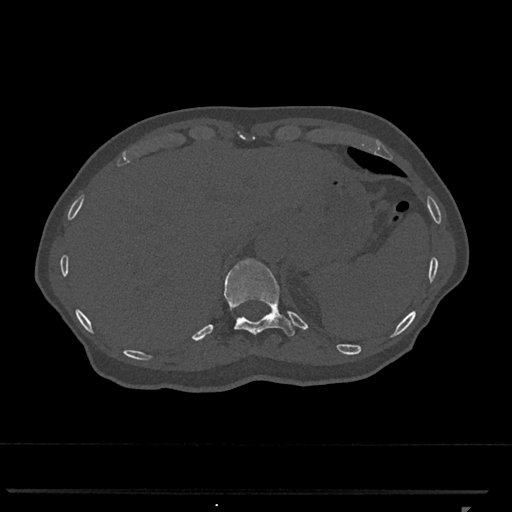
CT including the spine, one axial slice; position 517 of 793 along the scan axis; reconstruction kernel Br40s/3; 120 kVp; bone window (W 1800 / L 400 HU); 0.5 mm slice thickness; 512 × 512 image matrix, field of view 380 × 380 mm. Patient: female, 62 years. From the clinical record (not read from this slice): primary cancer: renal.
Annotated regions visible in this slice (semi-automatically segmented with operator editing):
- T11 vertebra: bounding box (x1, y1, x2, y2) in pixels: (224, 258, 295, 337)